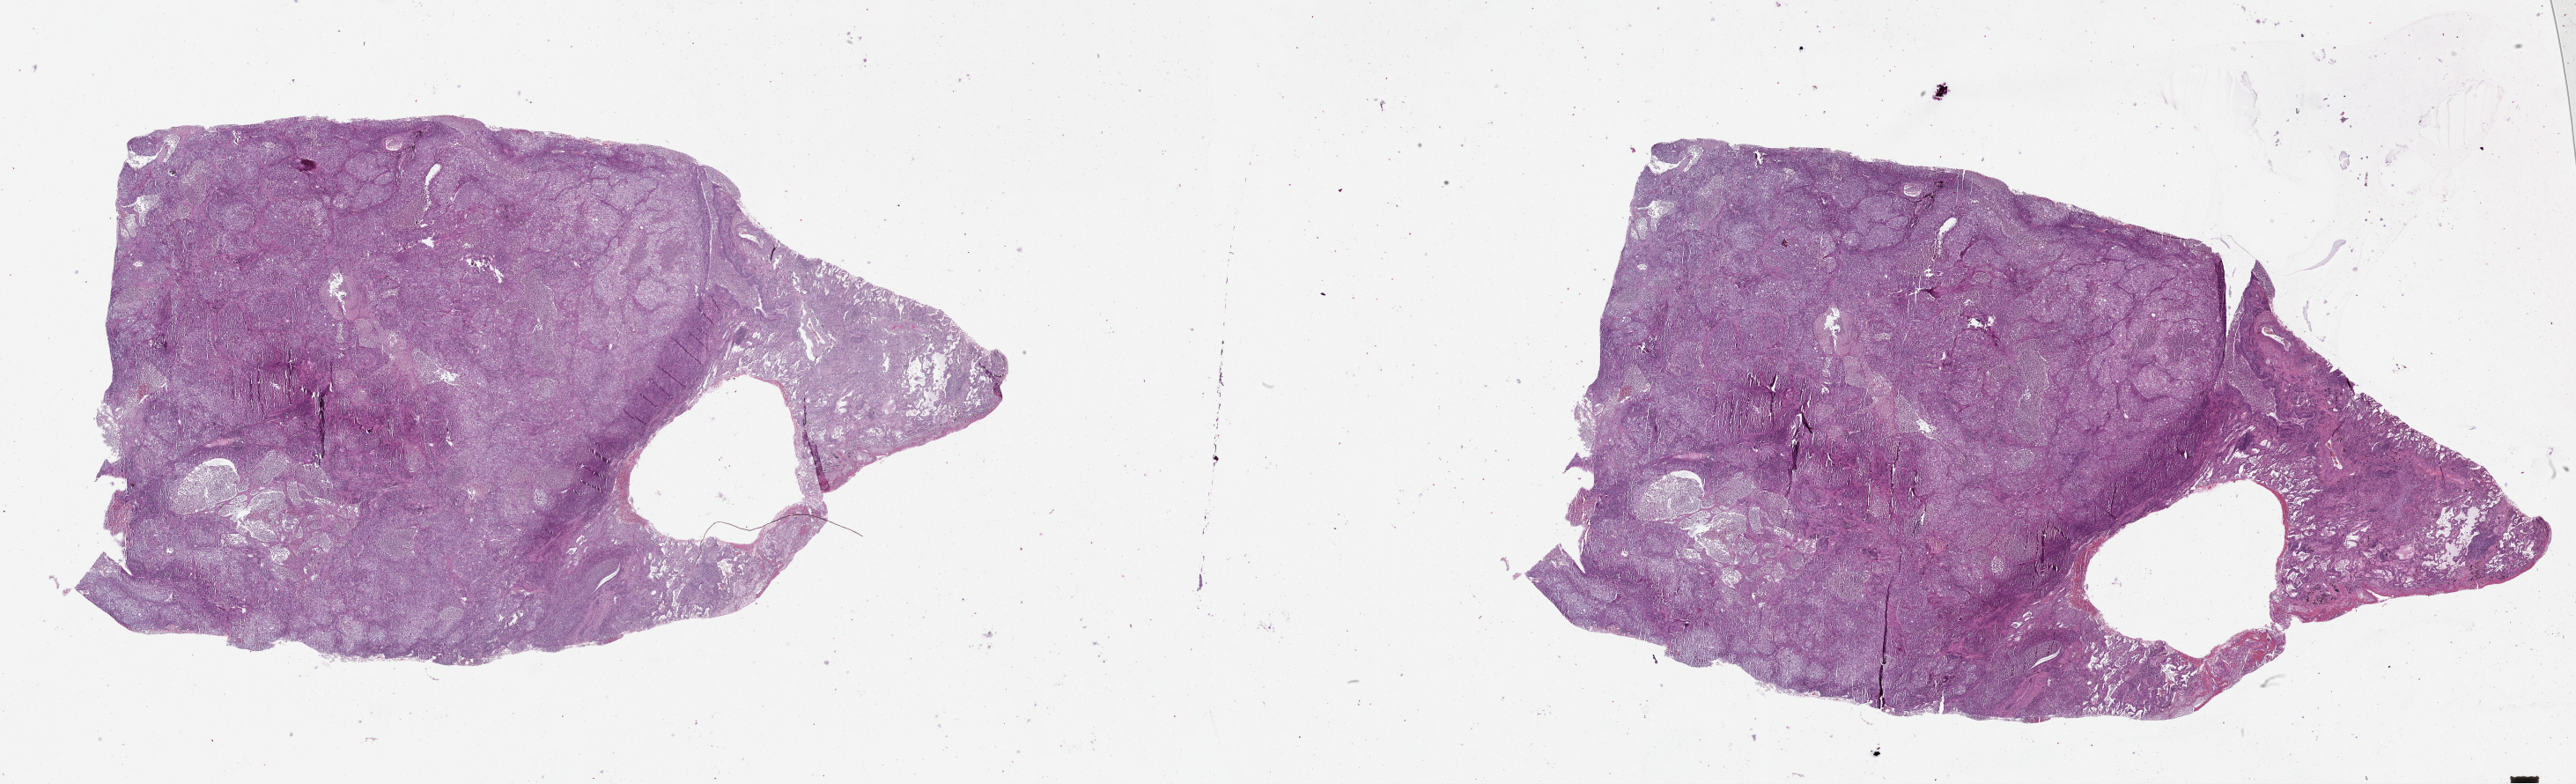
H&E whole-slide image, a low-resolution overview of the entire scanned area, about 47.1 x 14.3 mm (from a 20x scan), lung, tumour tissue. Female, 72 y/o.
- patient diagnosis (cohort enrolment): squamous cell carcinoma (lung)